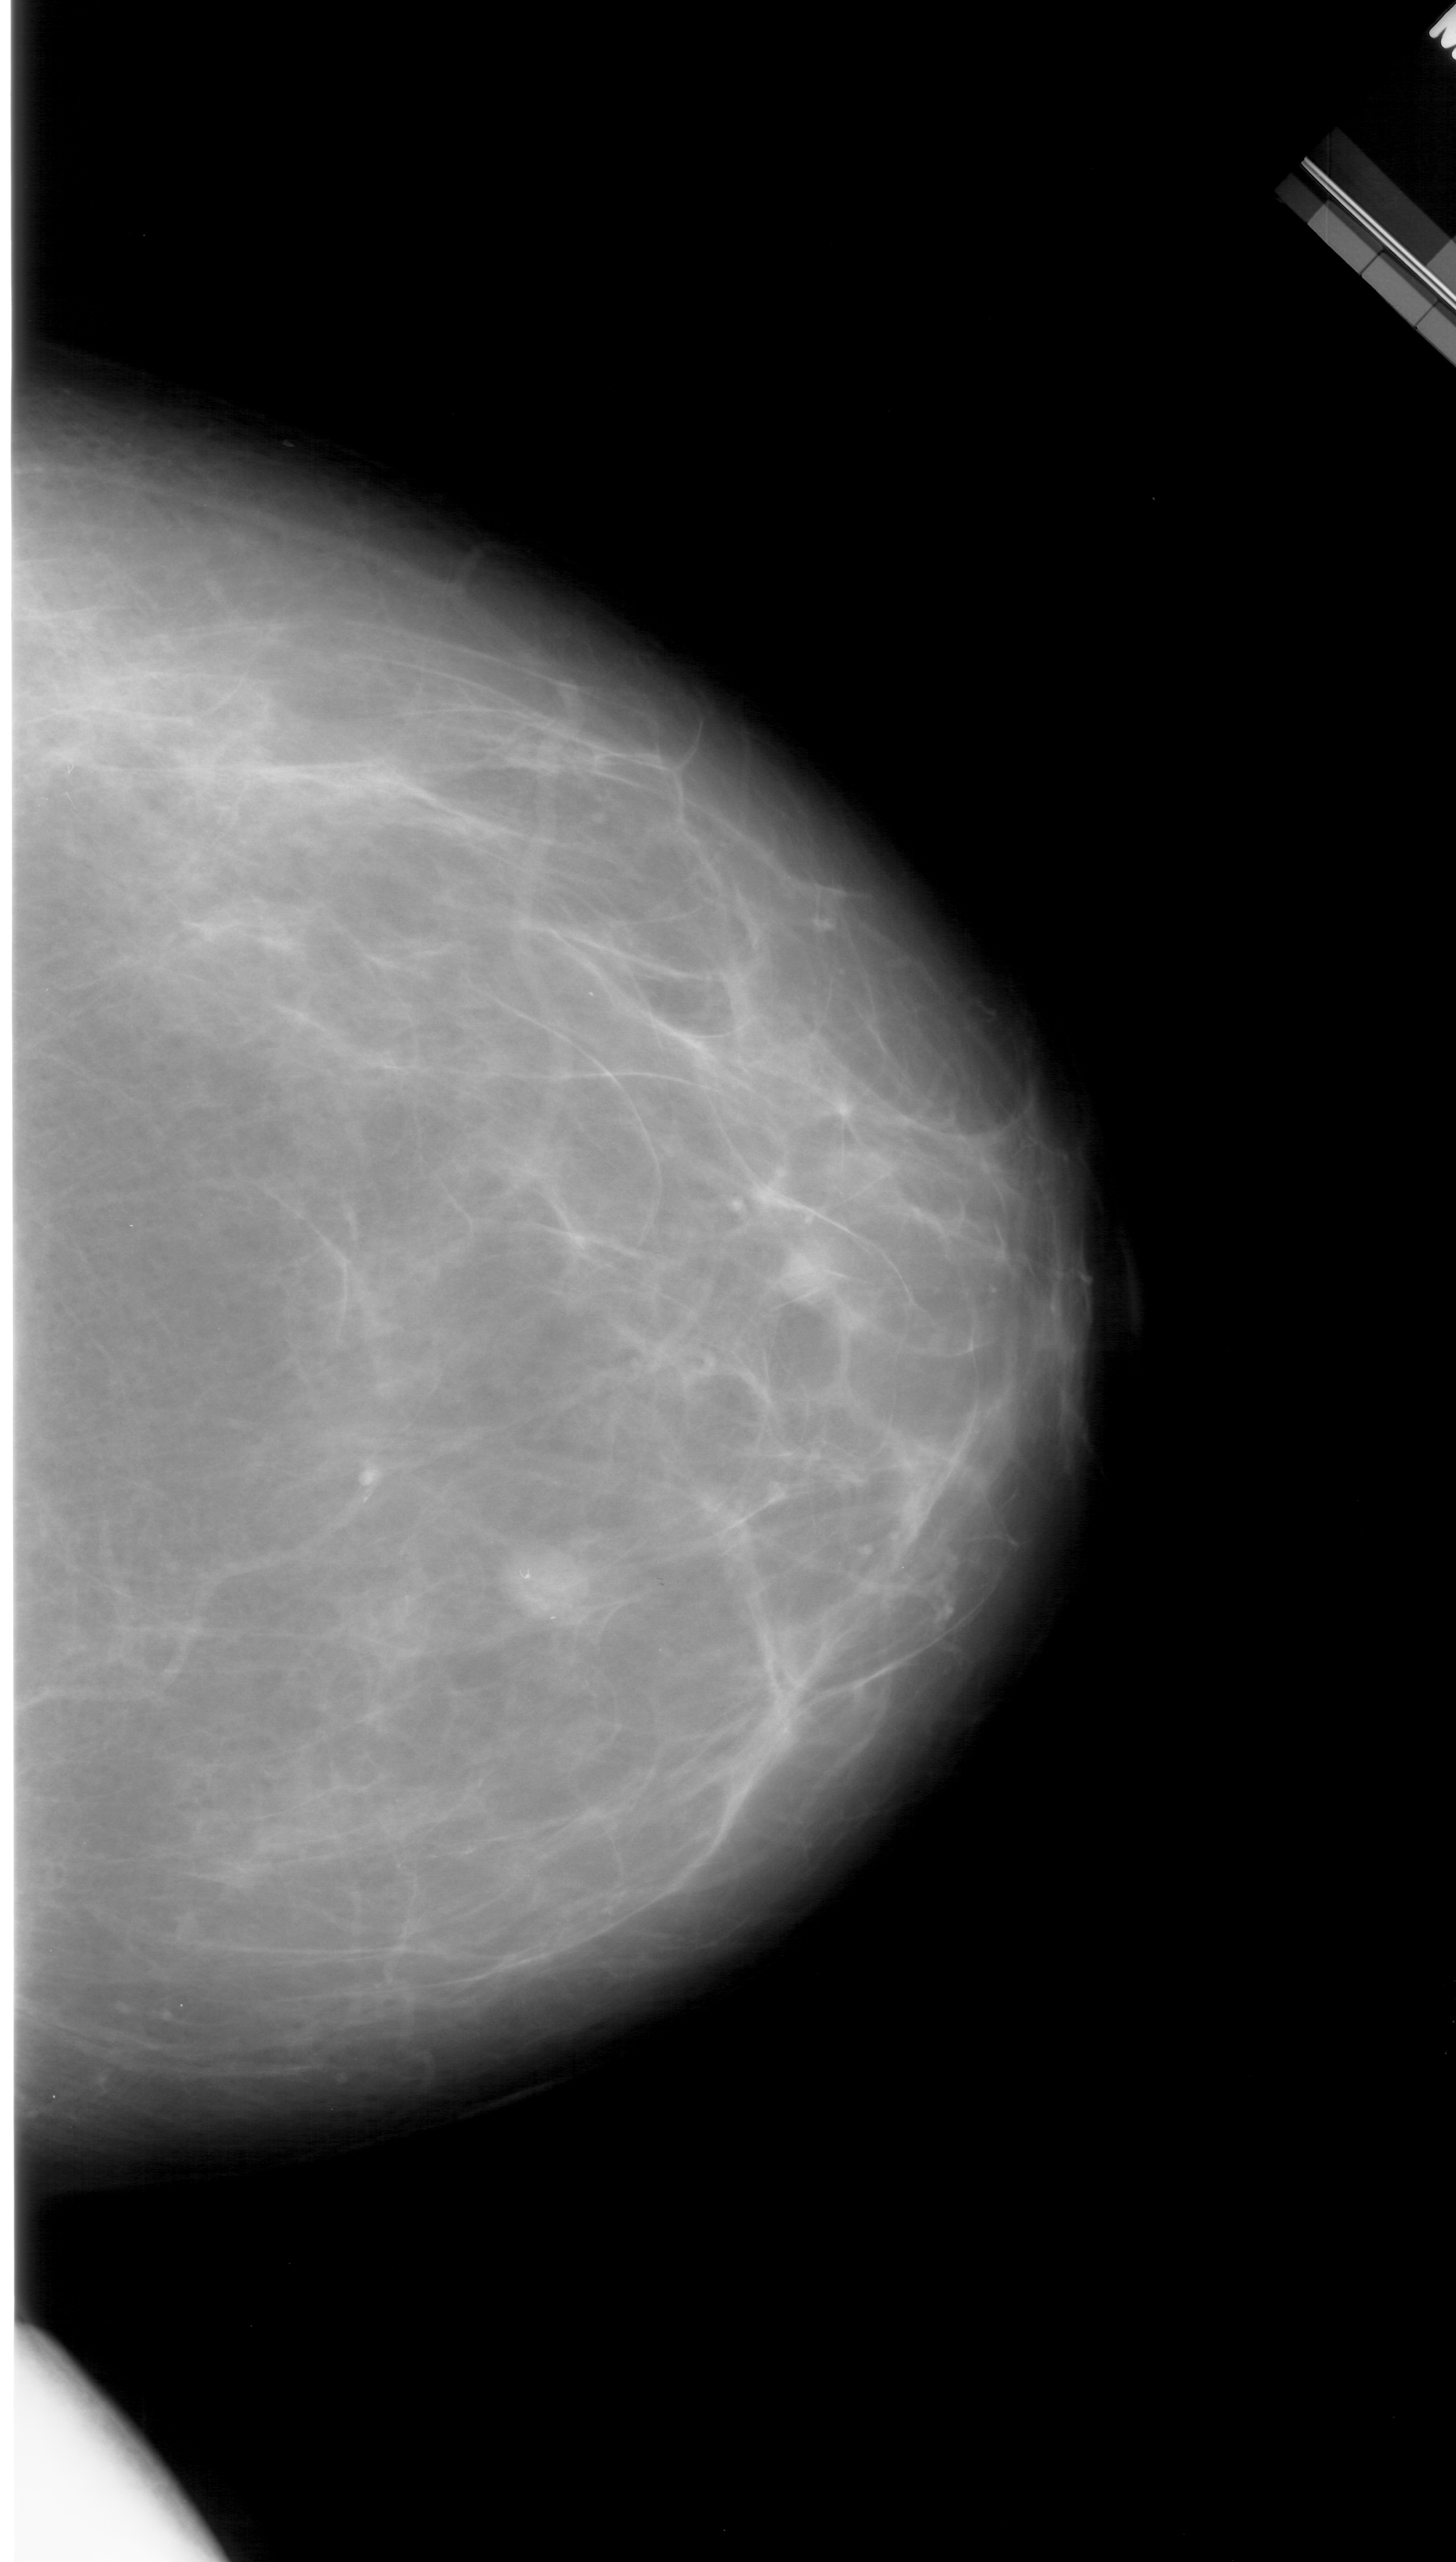
Scanned film-screen mammogram, right breast, CC view, BI-RADS breast density category 2 (scale 1–4).
- Marked findings (only marked abnormalities are described; nothing is implied about the rest of the image): mass, shape oval, margins circumscribed; BI-RADS assessment category 3; pathology (as recorded): benign.